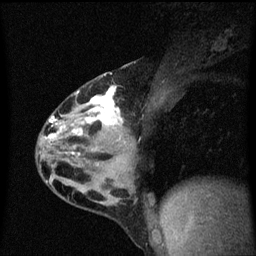
Breast MRI (dynamic contrast-enhanced), one sagittal slice. Position 34 of 60 along the scan axis. Dynamic contrast-enhanced series, image 2 of 3 at this slice position (ordered by acquisition). 1.5 T. TE 4.2 ms, TR 8.4 ms. 2 mm slice thickness. 256 × 256 image matrix, field of view 200 × 200 mm. Female patient, age 32 years.
Annotated regions visible in this slice (semi-automatically segmented with operator editing):
- analysis volume of interest (the breast-tissue region the enhancement analysis was run in; not a lesion): bounding box <36,74,151,169> (left, top, right, bottom; pixels)
- tumour enhancement mask (voxels above the 70 % enhancement threshold inside the analysis volume of interest): <49,86,125,157>